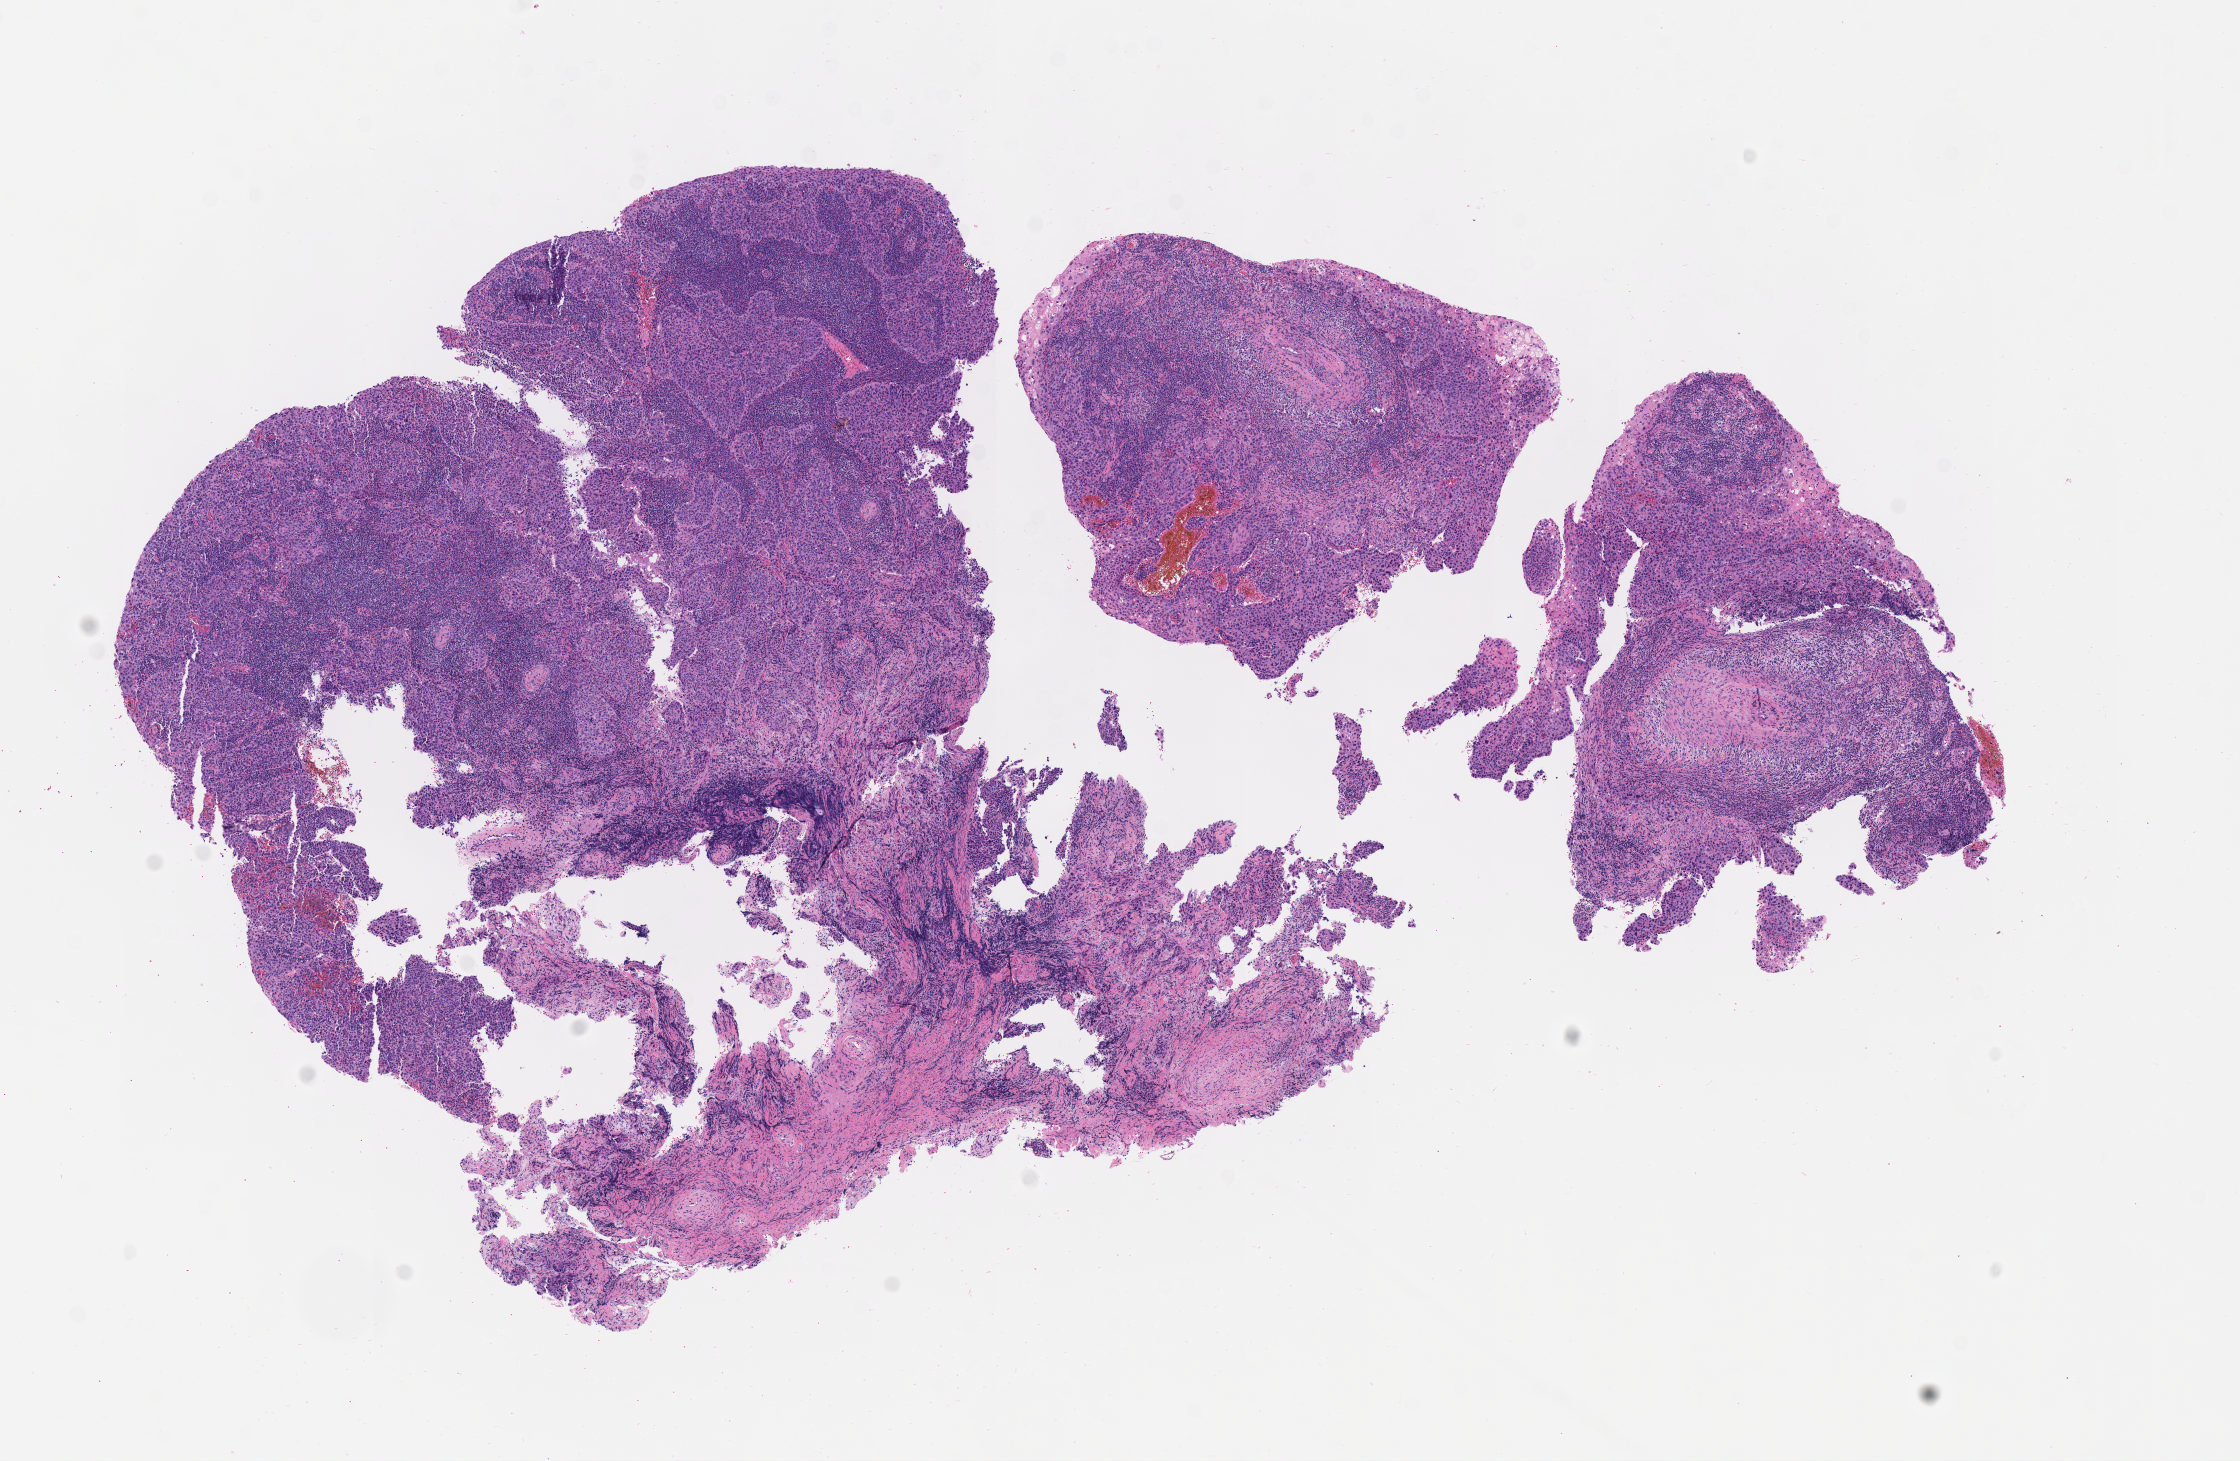
Whole-slide image, haematoxylin and eosin stain, a low-resolution overview of the entire scanned area, about 9.1 x 5.9 mm, specimen: tumor tissue, site: cervix. Patient female; age 43 years.
Histologic diagnosis: Squamous cell carcinoma, keratinizing, NOS.